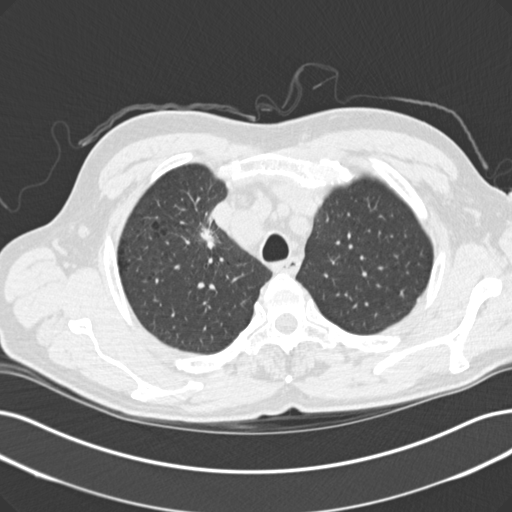
Low-dose screening chest CT, one axial slice. Slice 119 of 152 in the series (ordered by position). Reconstruction kernel B30f. Lung window (W 1500 / L -600 HU). 2 mm slice thickness. 512 × 512 image matrix, field of view 365 × 365 mm.
Structures marked on this image (outlined manually by an expert reader):
- lesion 1 (tumor, upper lobe of right lung): bounding box <200,228,215,249> (left, top, right, bottom; pixels)